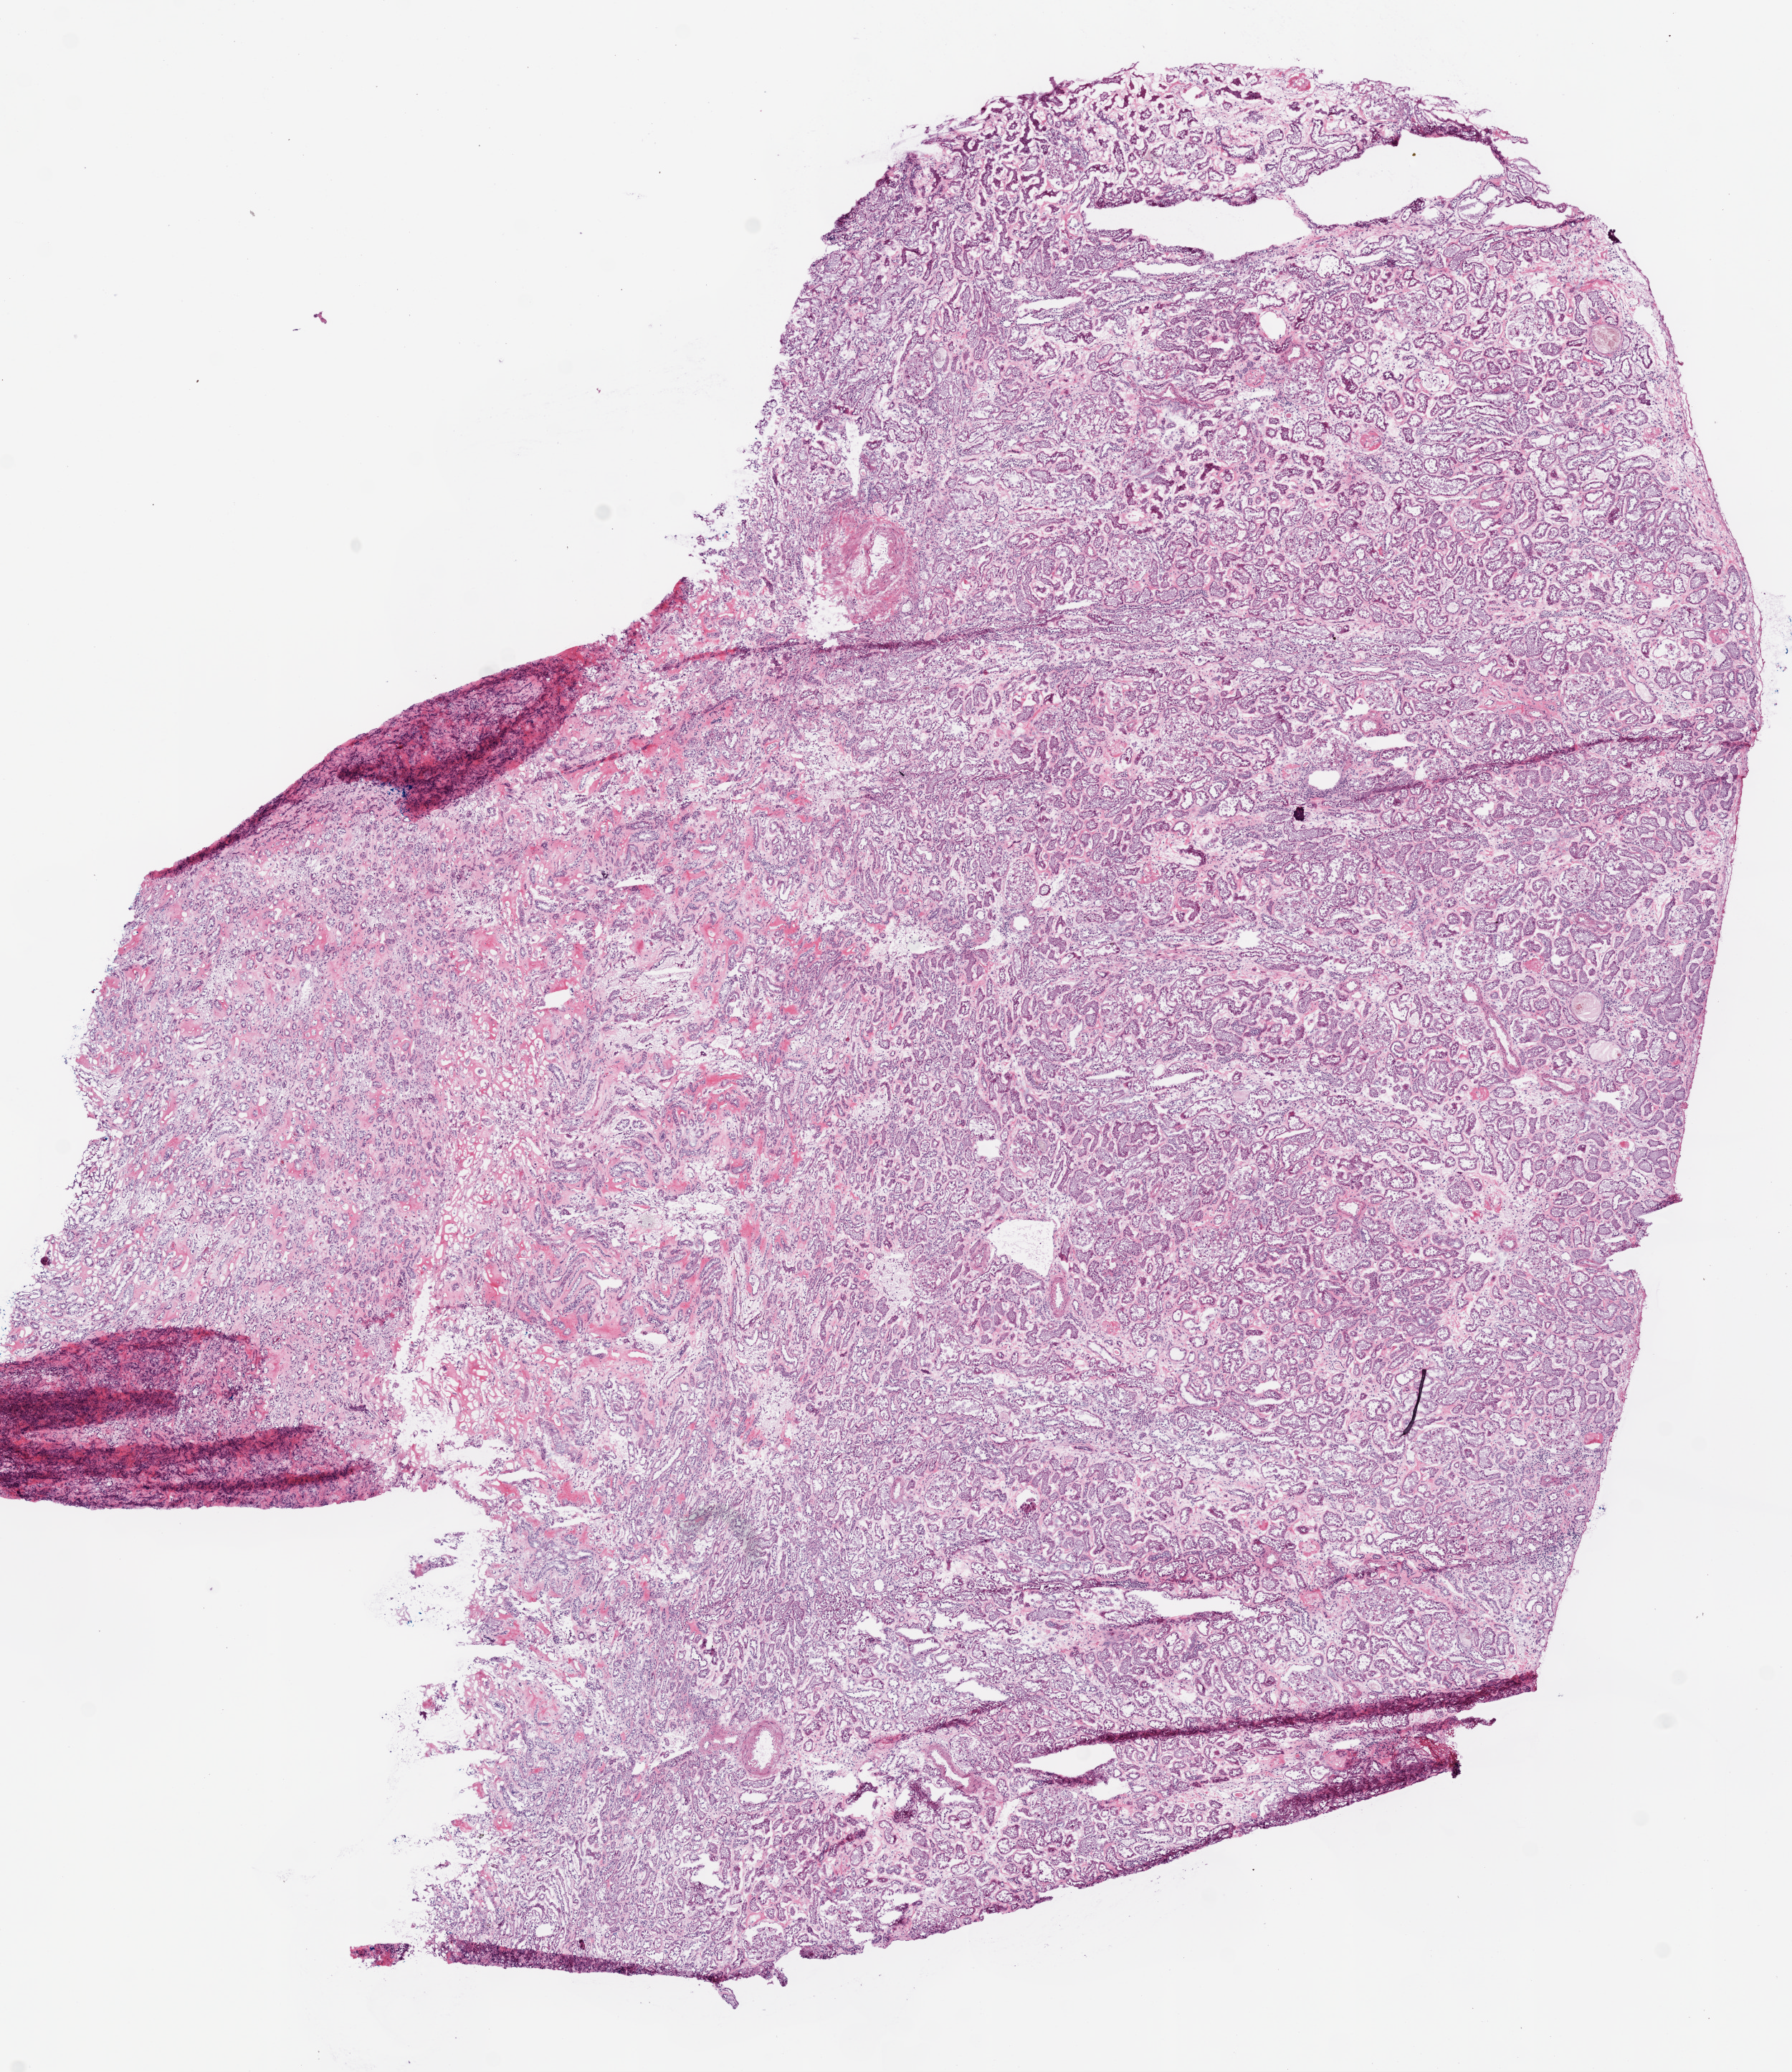
Digitized H&E-stained tissue section (whole slide), a low-resolution overview of the entire scanned area, about 10.0 x 11.6 mm (slide scanned at 20x); frozen section; kidney, solid tissue normal (non-tumour tissue) sample. Patient: male, age at initial diagnosis 79 years.
This section: solid tissue normal (non-tumour) sample from the same patient. Patient diagnosis: Clear cell adenocarcinoma, NOS.